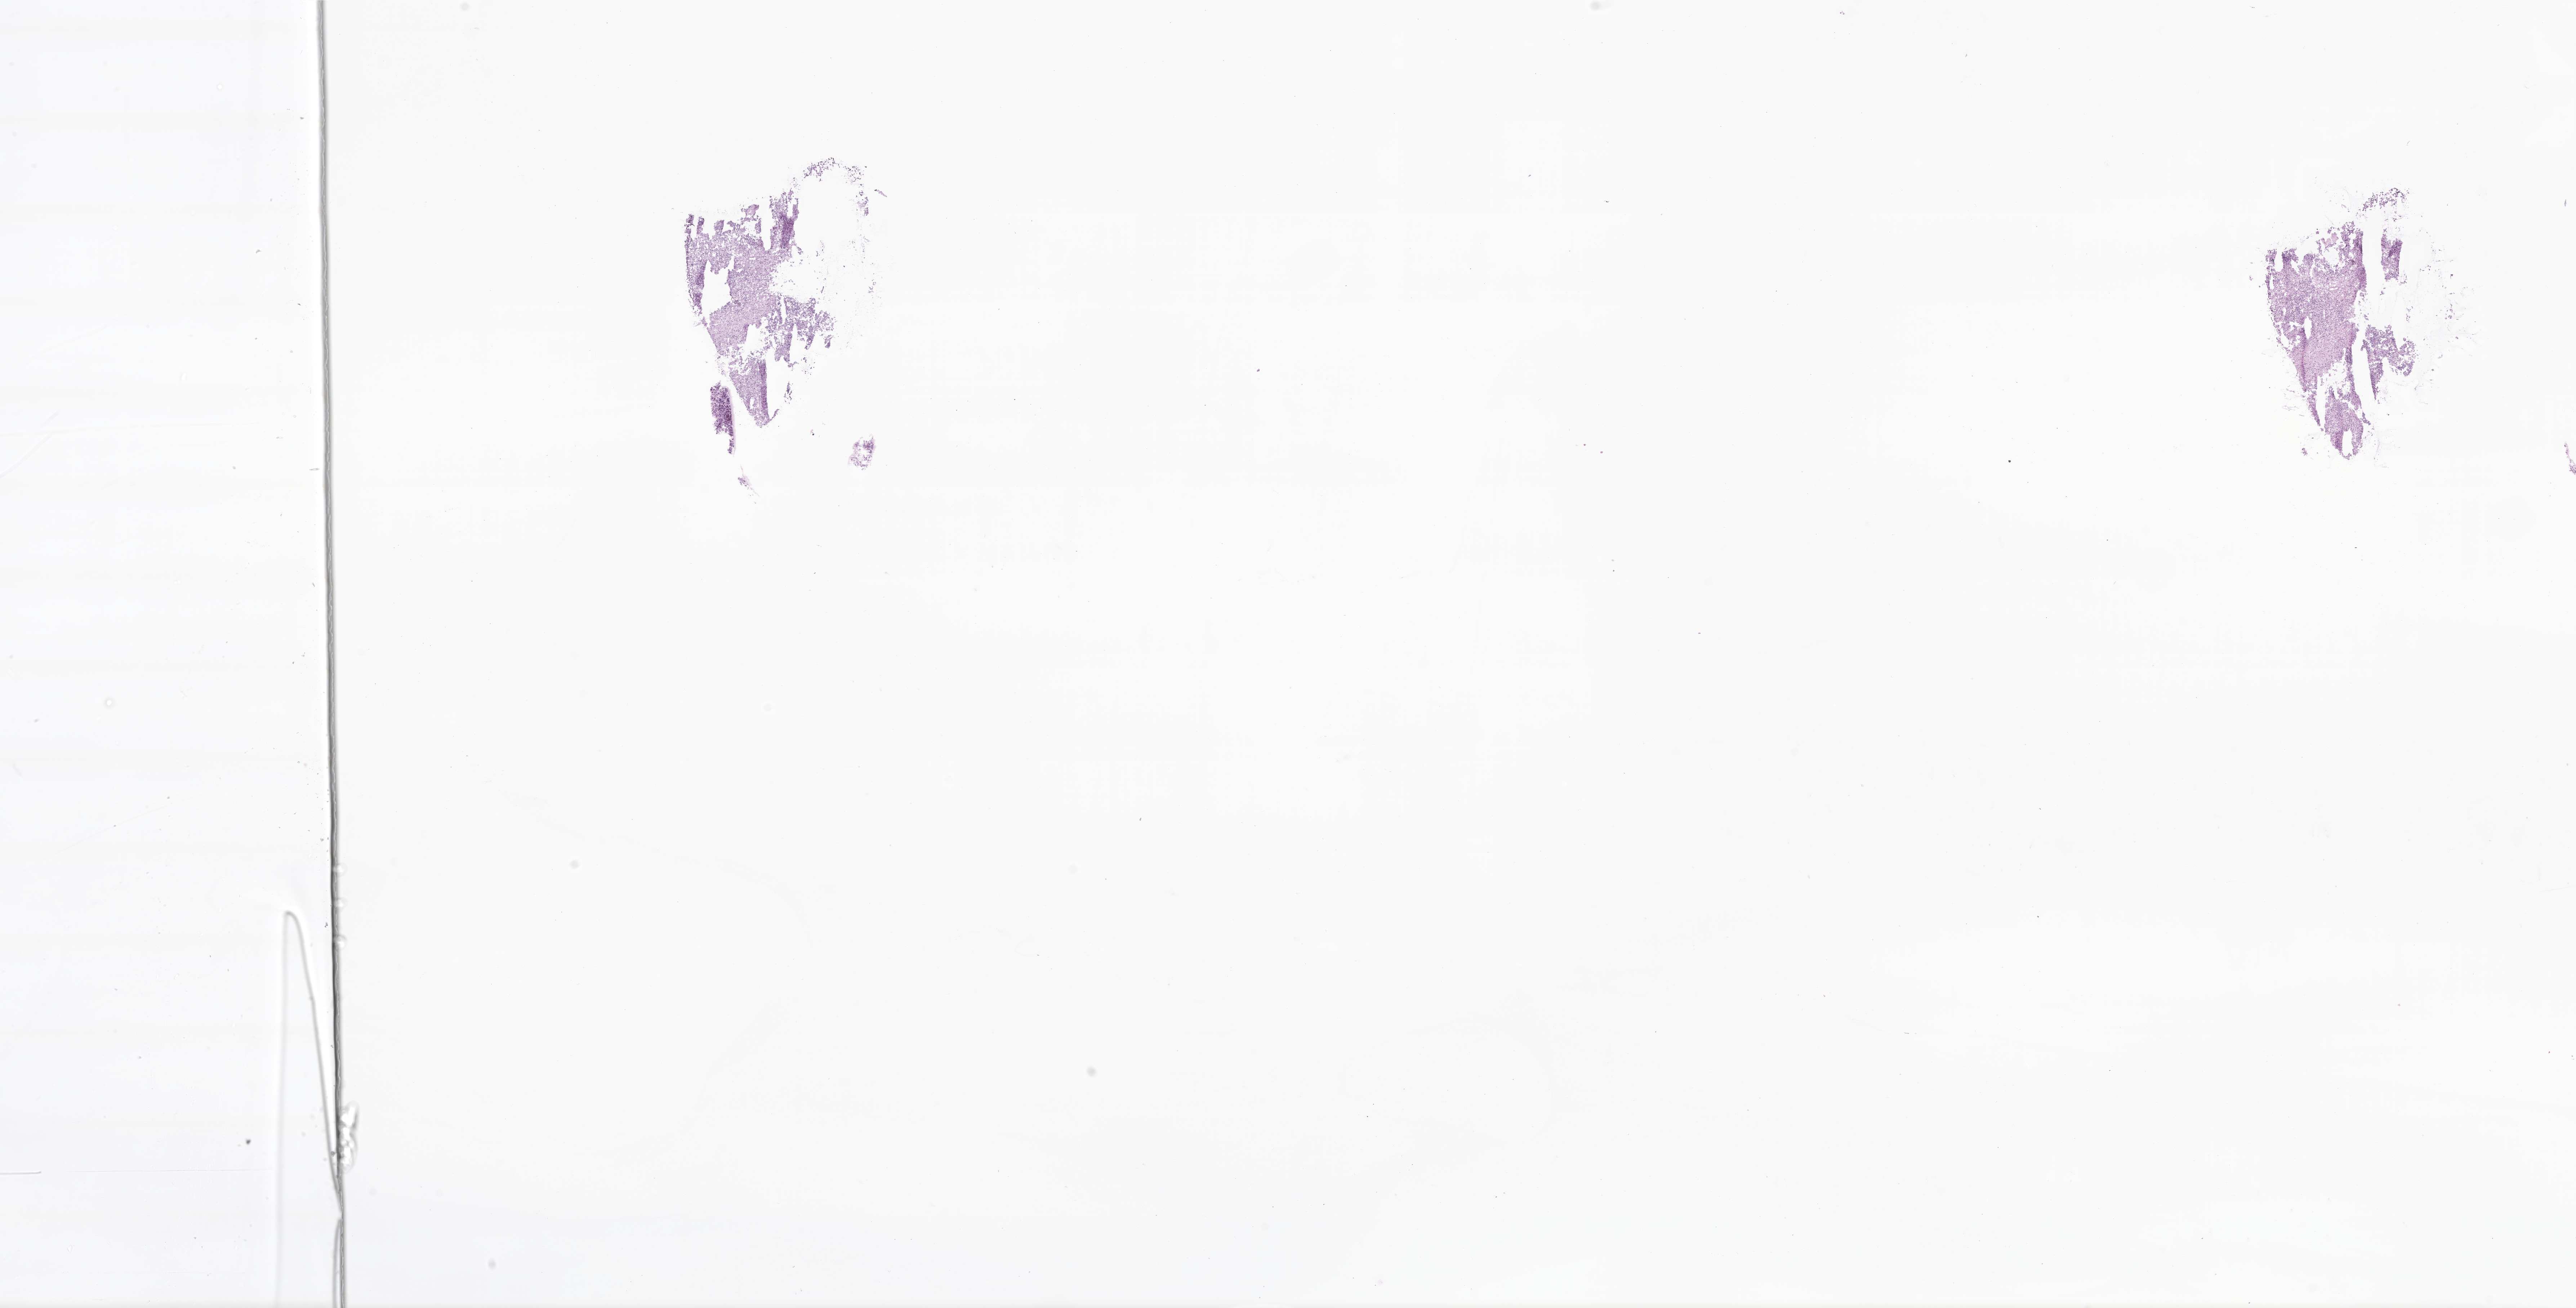
Digitized H&E-stained section of tumor tissue from the adrenal gland — whole scanned area (about 30.1 x 15.3 mm) shown as a low-resolution overview, frozen section (OCT-embedded). Patient: female, age 331 days.
Diagnosis: Neuroblastoma, NOS.